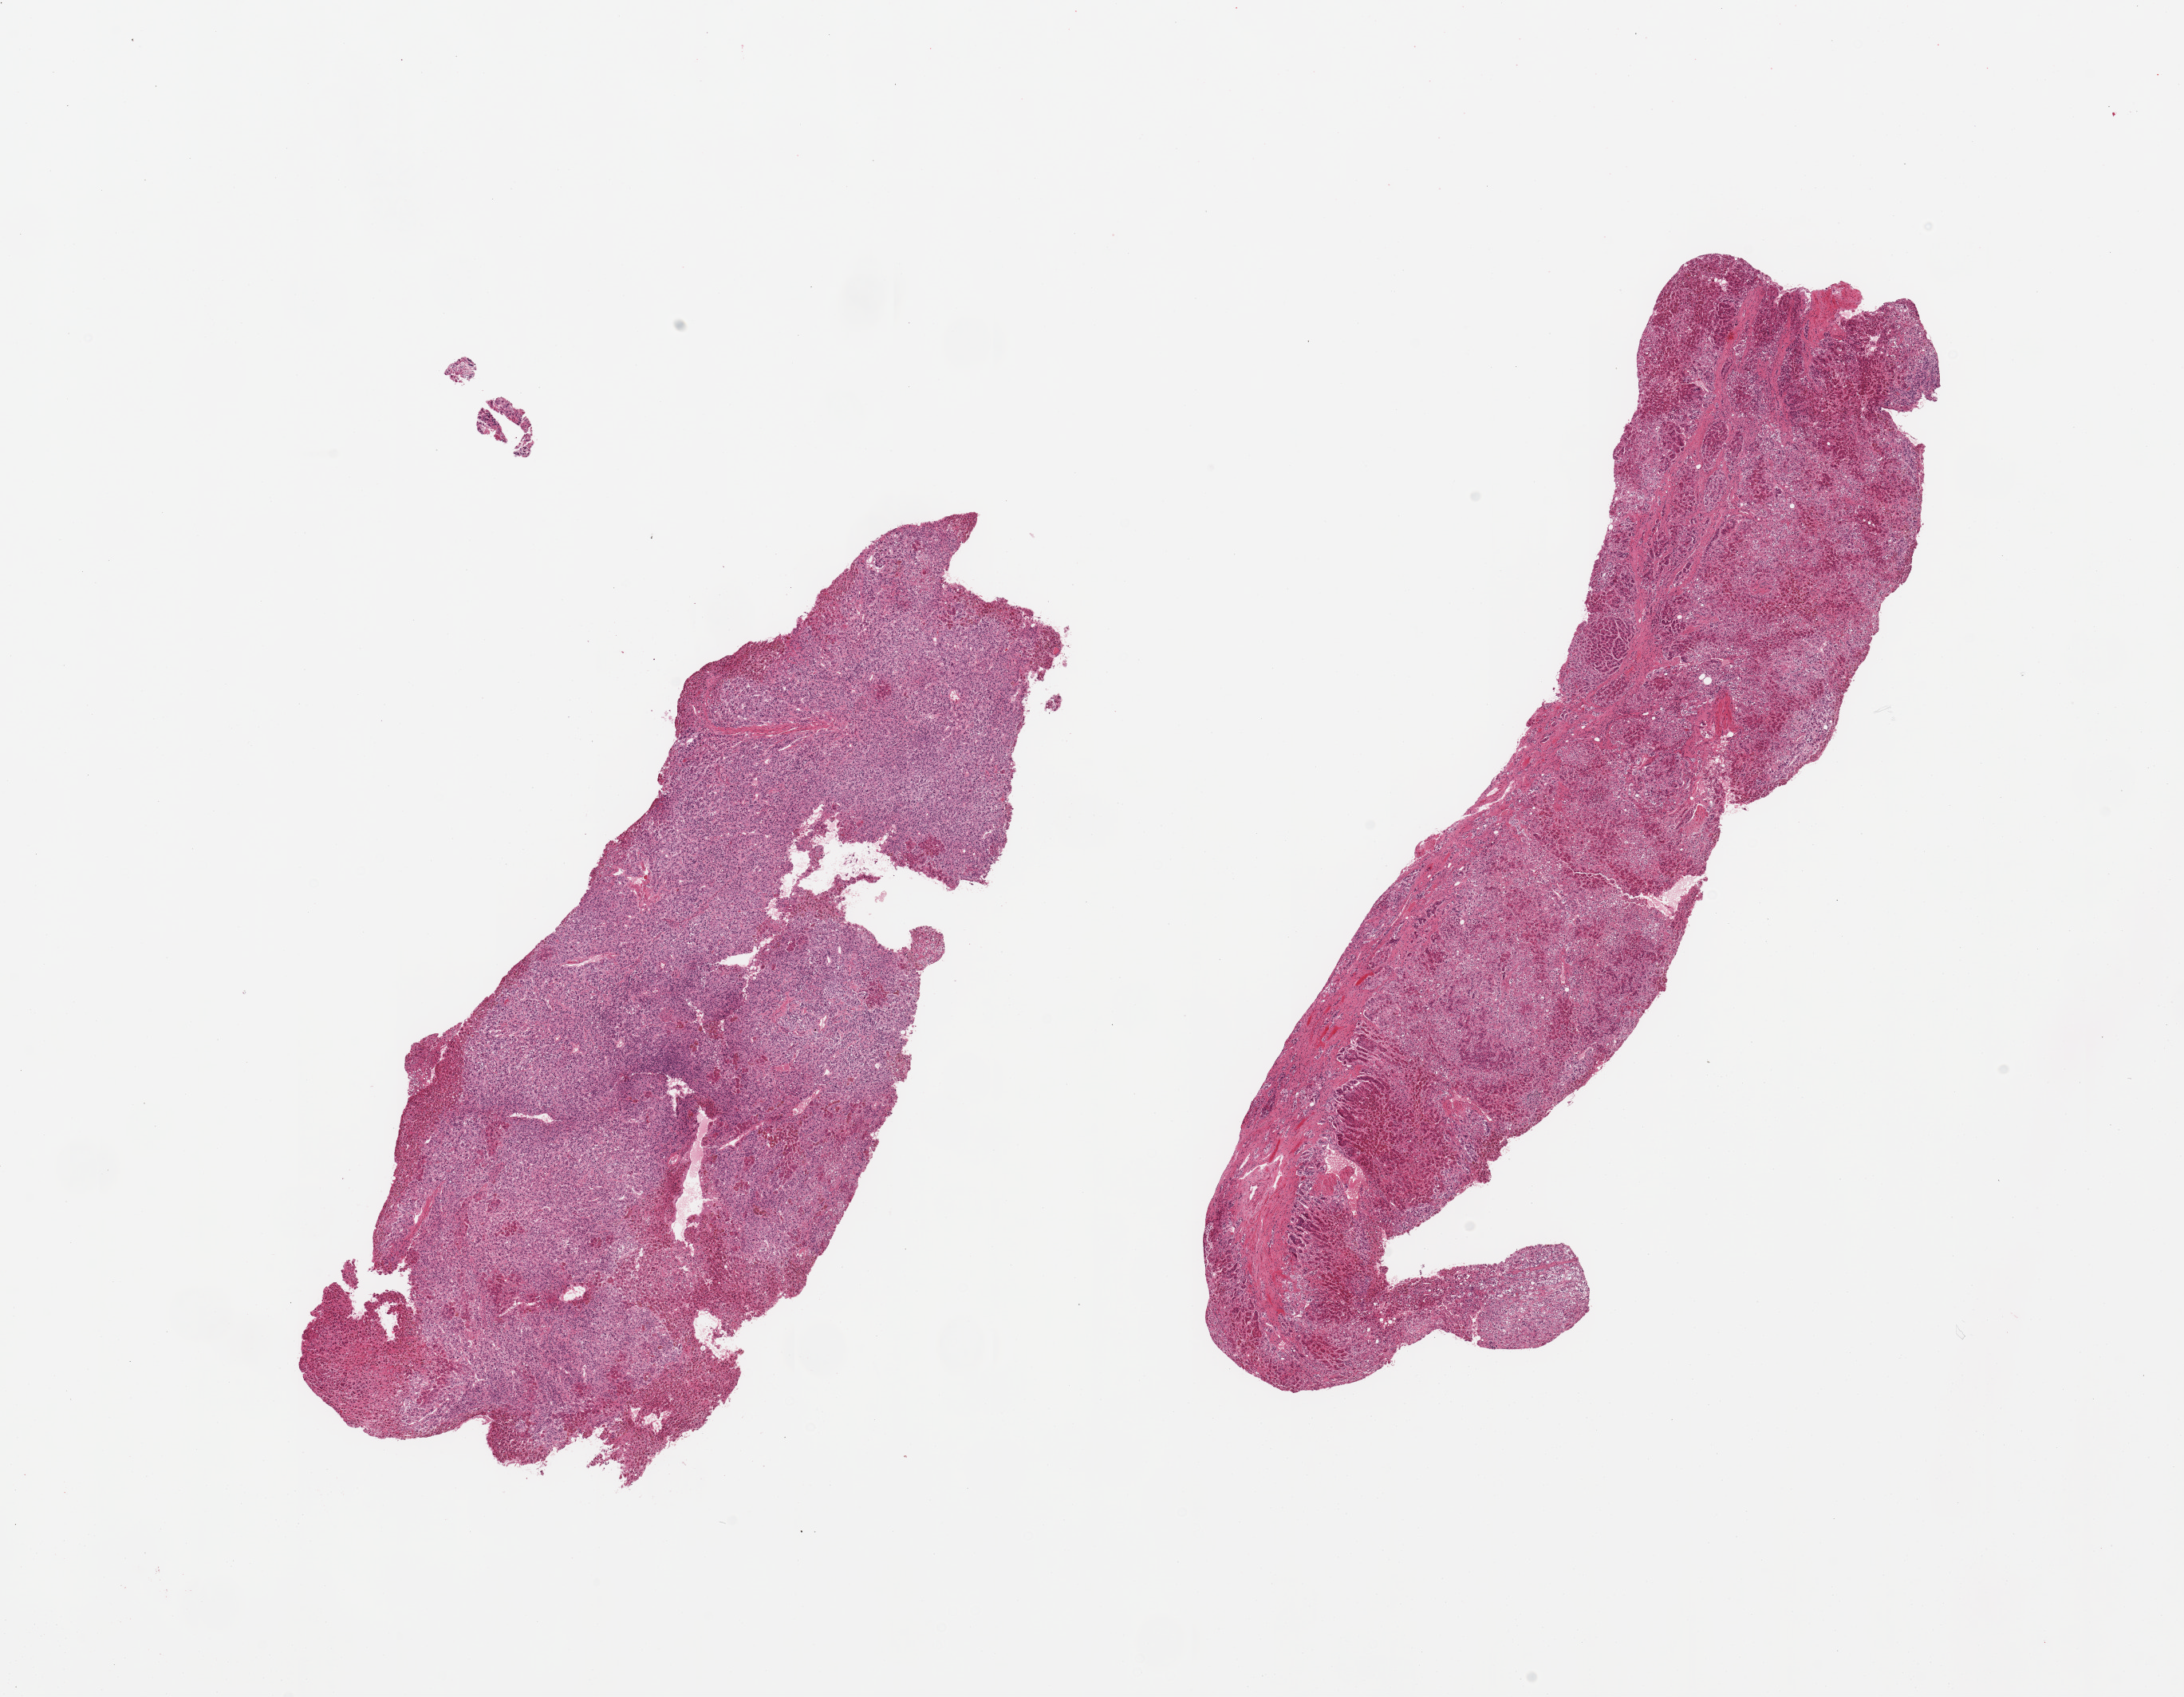
Digitized haematoxylin and eosin-stained section, low-resolution overview of the scanned area, about 21.7 x 16.8 mm. PAXgene-fixed, paraffin-embedded tissue. Target tissue: adrenal gland. Donor tissue sample. Male donor.
- reviewer comment on this tissue sample: 2 pieces; well dissected: no fat